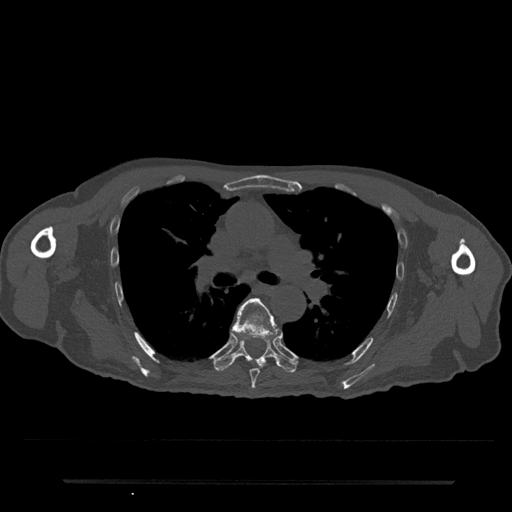
CT including the spine, one axial slice. Slice 506 of 797 in the series (ordered by position). Reconstruction kernel Br40s/3. 120 kVp. Bone window (W 1800 / L 400 HU). 512 × 512 image matrix, field of view 427 × 427 mm. Patient: male, 74 years. From the clinical record (not read from this slice): primary cancer: prostate.
Annotated regions visible in this slice (semi-automatic segmentation, software-assisted and operator-edited):
- T6 vertebra: bounding box (x1, y1, x2, y2) in pixels: (231, 298, 279, 389)
- T7 vertebra: (215, 340, 297, 372)